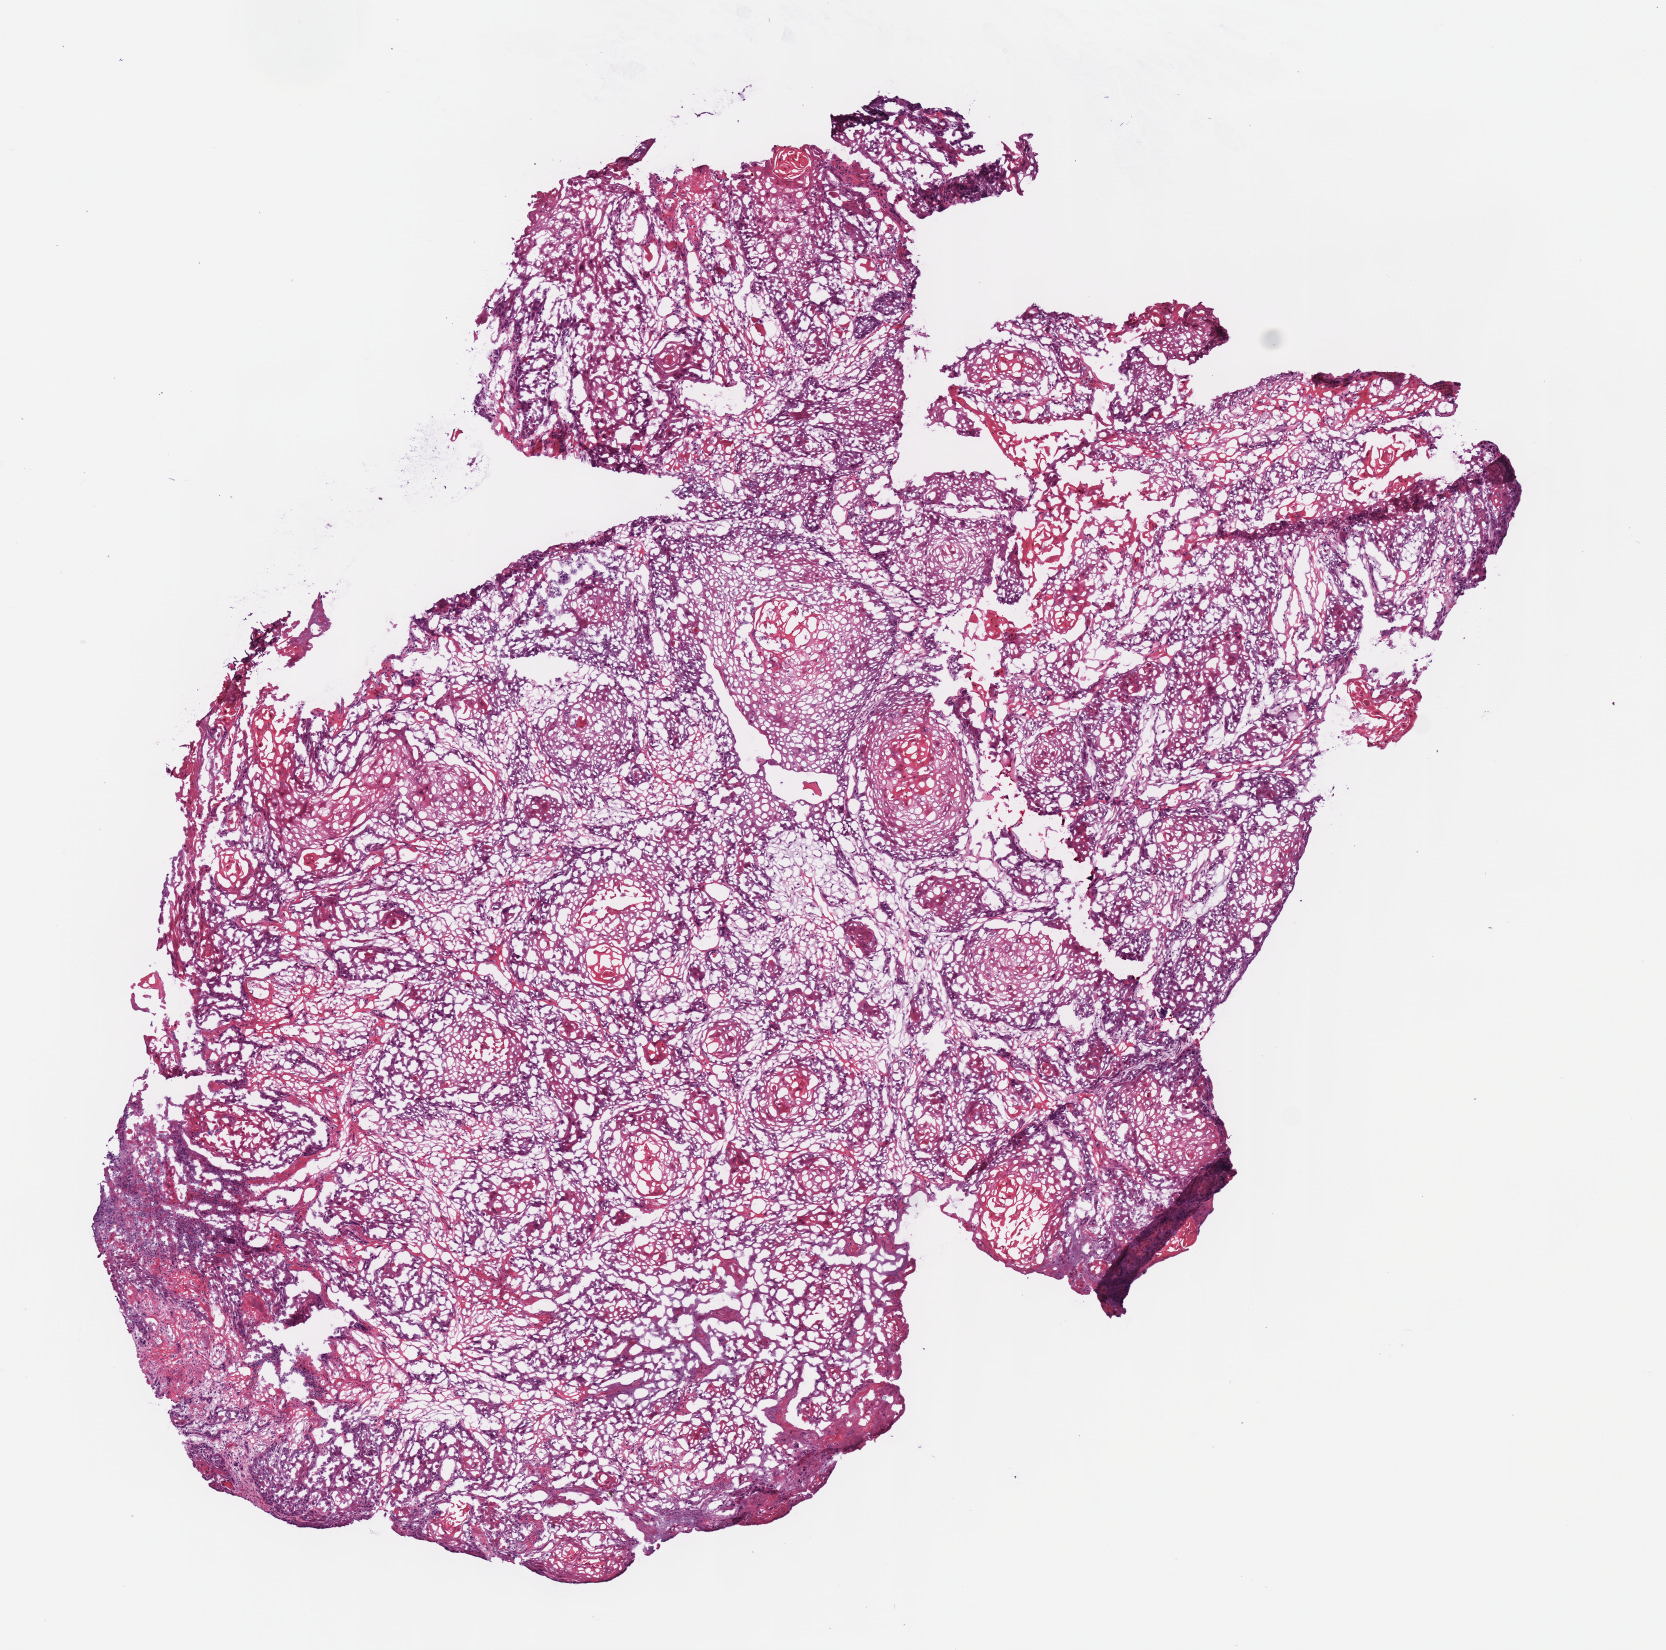
Whole-slide histology image, H&E-stained, whole scanned area (about 6.6 x 6.5 mm, acquisition: 40x scan) shown as a low-resolution overview, frozen section, sample: primary tumour, head and neck. Male, age 65 years at initial diagnosis. Histologic grade: G1 (well differentiated). Pathologist review of this section (percent, as recorded): tumour cells 100%, tumour nuclei 80%, normal cells 0%, stromal cells 0%, necrosis 0%. Inflammatory infiltration, as recorded: lymphocyte infiltration 5%, monocyte infiltration 0%, neutrophil infiltration 5%.
* TNM: T2 NX
* AJCC pathologic stage: II (7th edition)
* diagnosis: Squamous cell carcinoma, NOS (overlapping lesion of lip, oral cavity and pharynx)